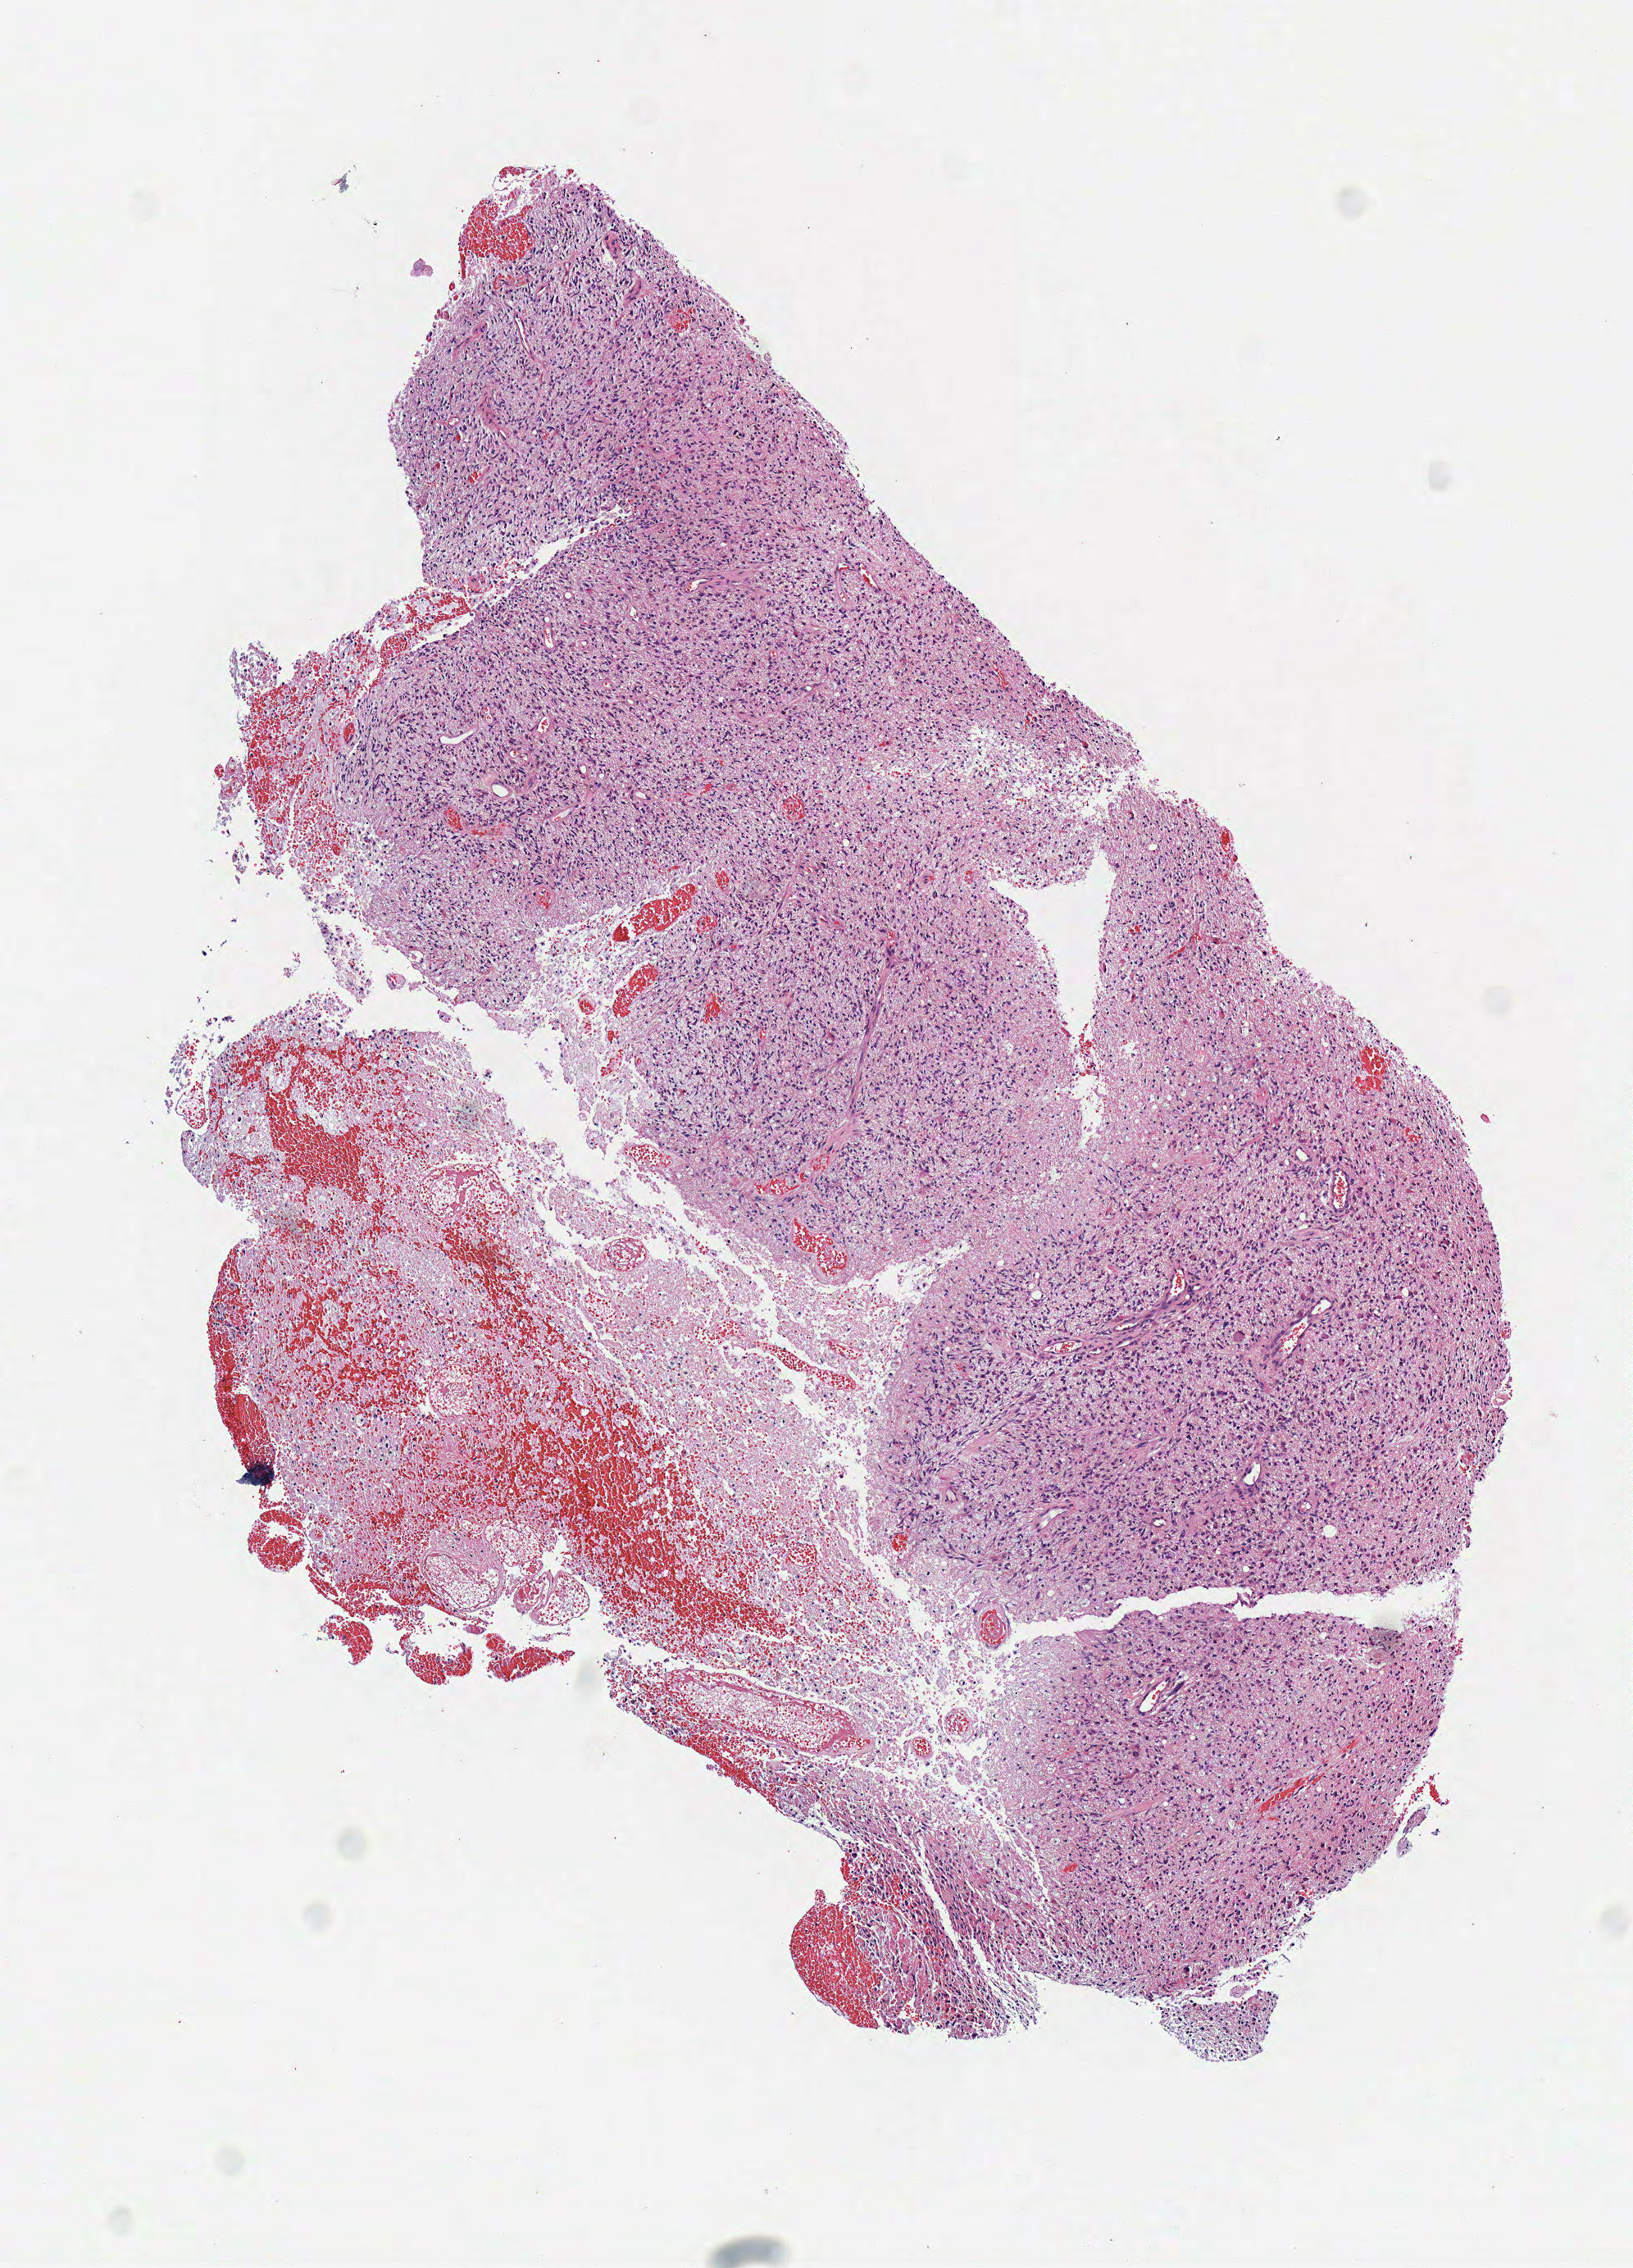
Whole-slide histology image, H&E-stained, low-resolution overview of the scanned area, about 3.9 x 5.4 mm (acquisition: 40x scan); frozen section; sample: primary tumour, brain. Male patient; age at initial diagnosis 64 years. Composition of this section per pathologist review: tumour cells 100%, tumour nuclei 75%, normal cells 0%, stromal cells 0%, necrosis 0%.
Histologic diagnosis: Glioblastoma.